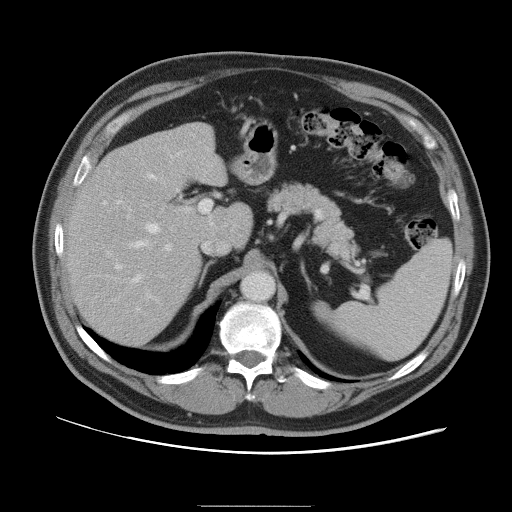
Contrast-enhanced abdominal CT, one axial slice. Slice 65 of 105 in the series (ordered by position). 120 kVp. Soft-tissue window (W 400 / L 40 HU). 512 × 512 image matrix, field of view 399 × 399 mm. Male patient, age 64 years. Case-level facts recorded for this patient, not image findings: diagnosis: colorectal cancer liver metastases, imaged before liver resection; multiple liver metastases: yes; largest metastasis: 3 cm.
Structures marked on this image (manually delineated by an expert):
- hepatic veins: box from (x=134, y=175) to (x=160, y=282) px
- liver: (x=67, y=124)–(x=252, y=345)
- planned liver remnant (the part of the liver to remain after resection): (x=67, y=137)–(x=251, y=345)
- portal vein (with intrahepatic branches): (x=115, y=200)–(x=212, y=310)